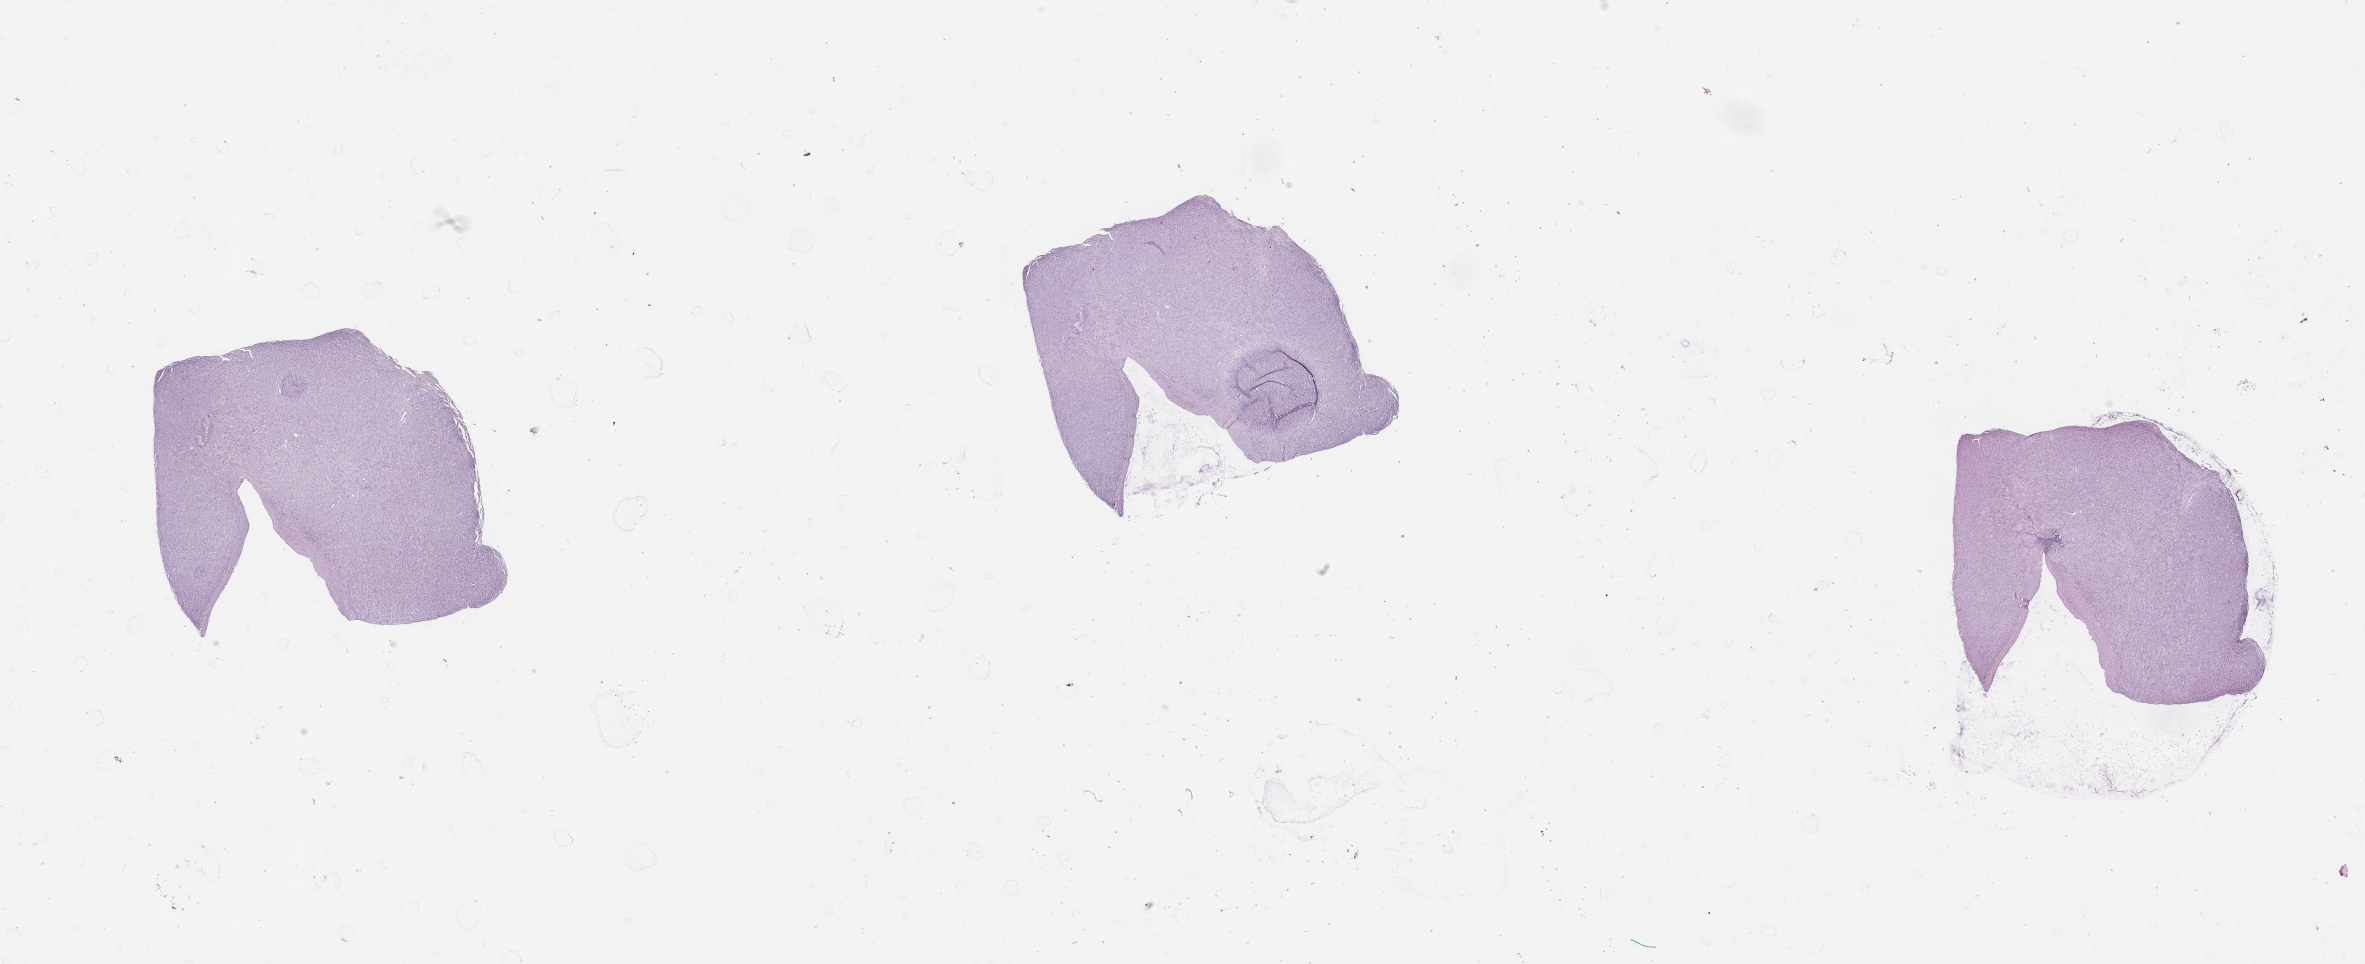
Whole-slide histology image, H&E, a low-resolution overview of the entire scanned area, about 37.4 x 15.2 mm; tumour tissue sample, sampled site: lung. 51-year-old male patient. Histologic grade: G2 (moderately differentiated). Slide review estimates, as recorded: tumour nuclei 85%, necrosis 0%.
AJCC pathologic stage: IIB. Histologic diagnosis: Squamous cell carcinoma, NOS. Primary tumour site (as recorded): right middle lobe.